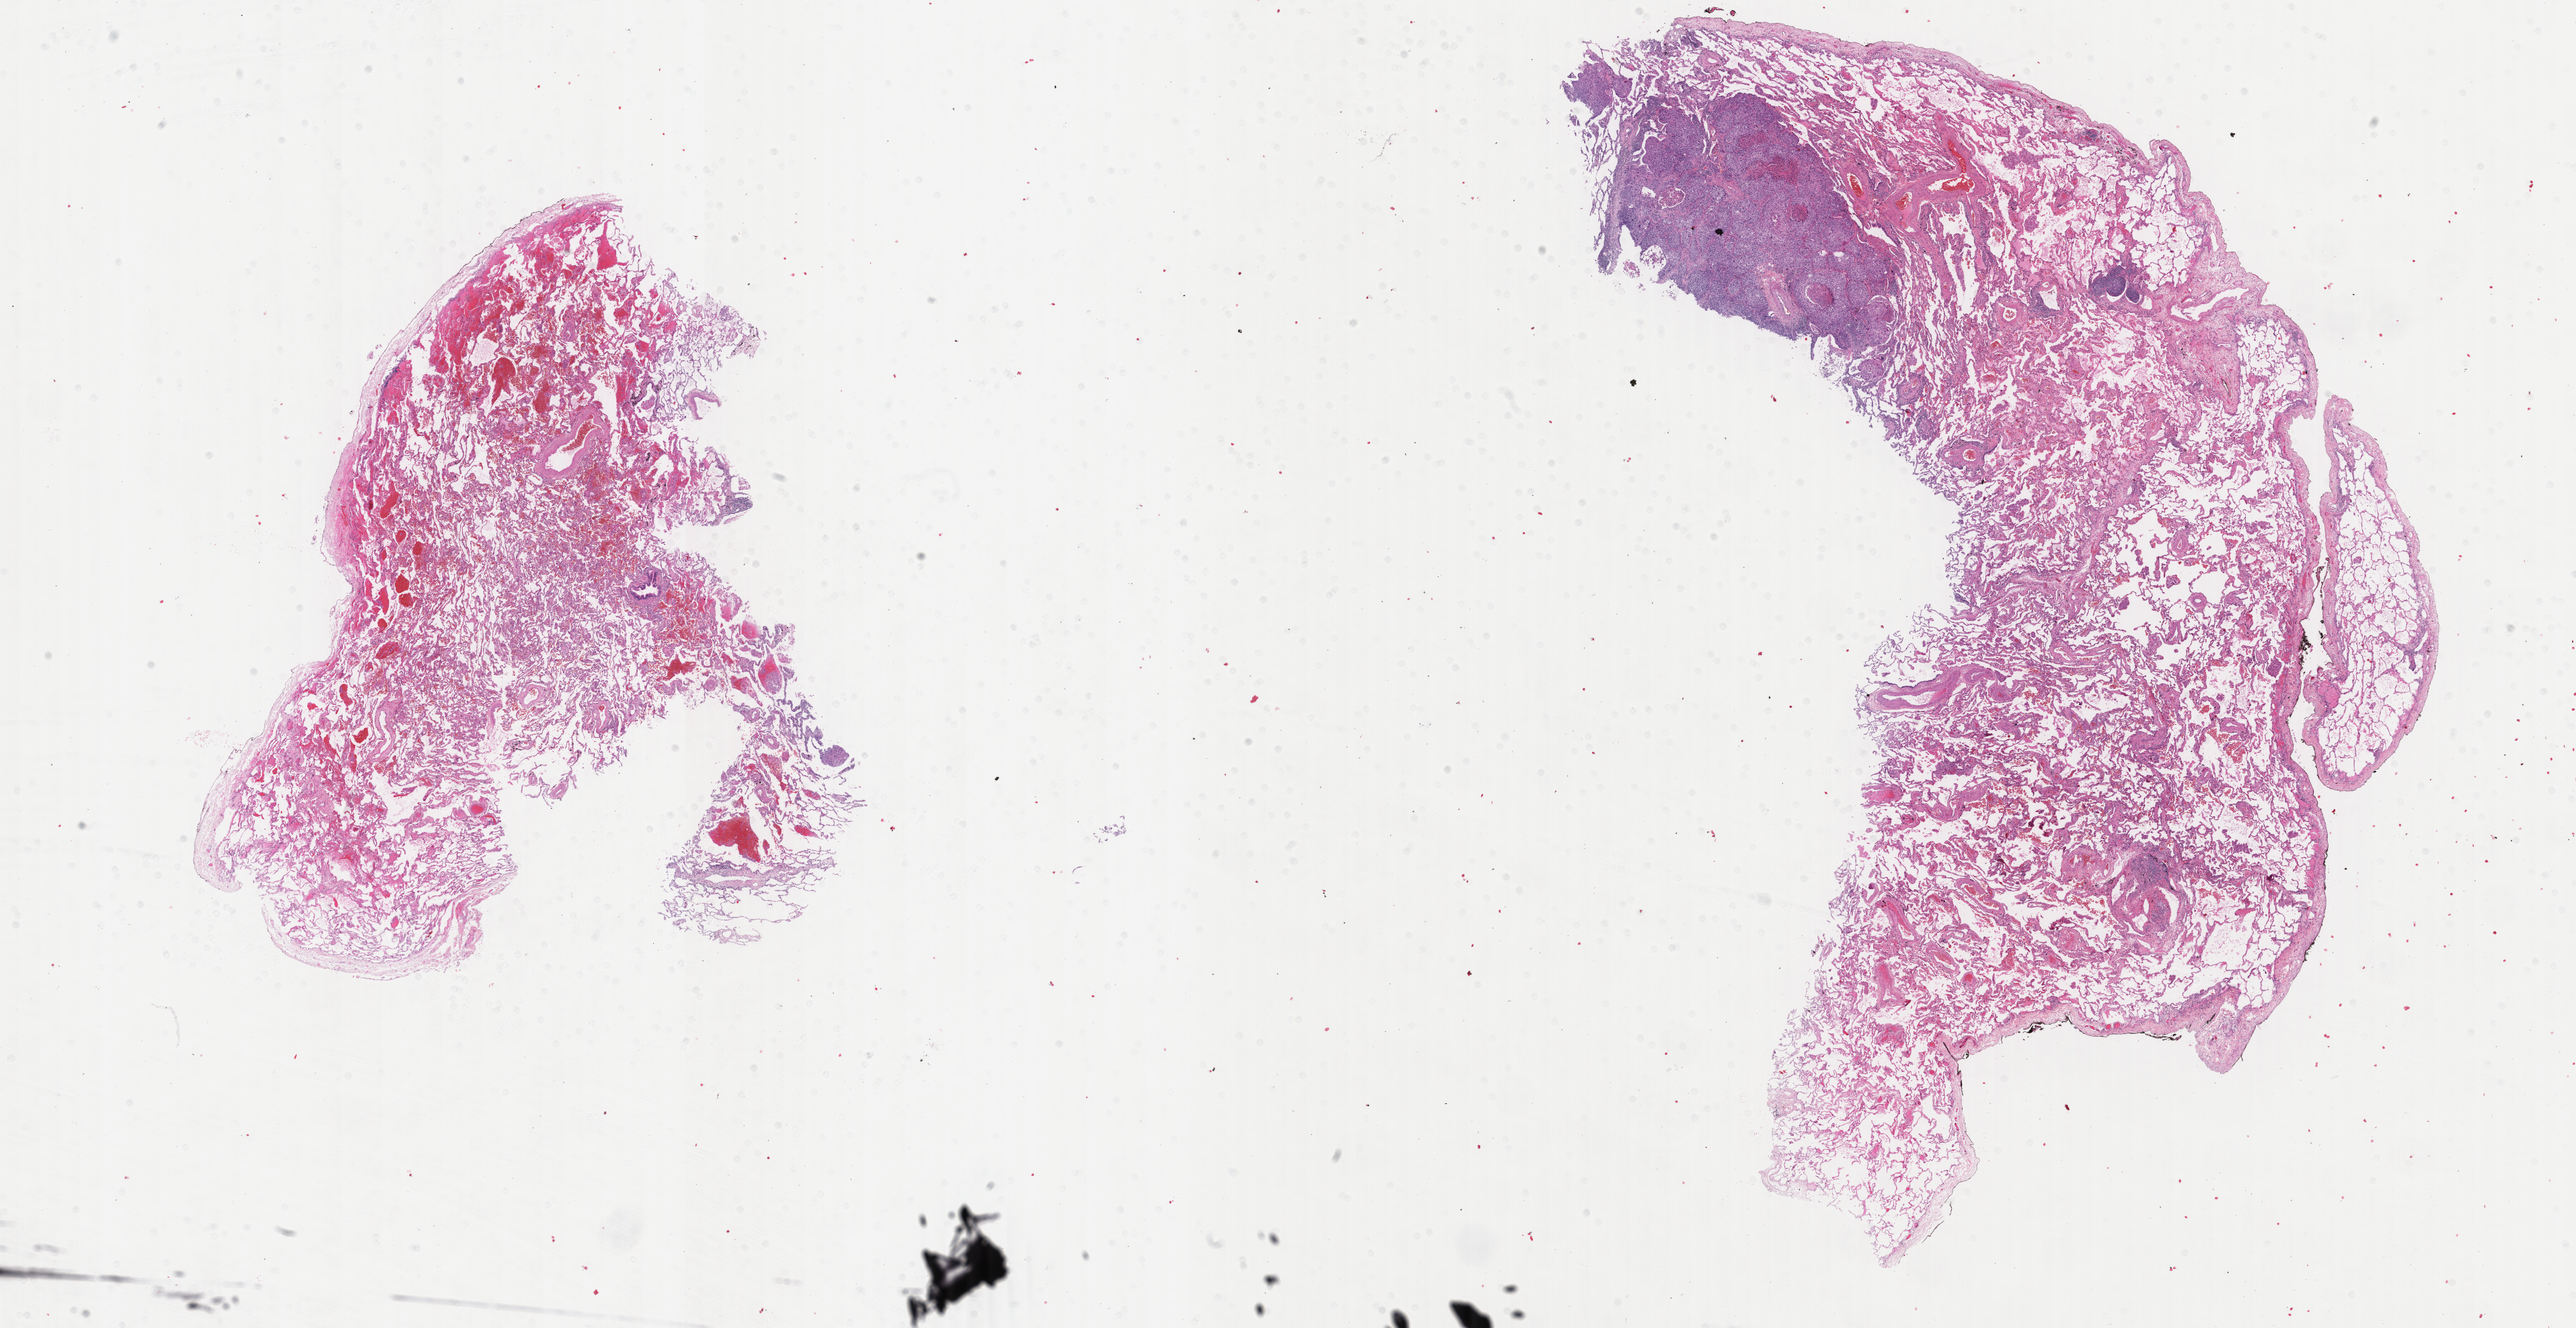
Digitized H&E tissue section (whole slide) — a low-resolution overview of the entire scanned area, about 30.5 x 15.7 mm; formalin-fixed paraffin-embedded (FFPE) diagnostic section; lung, primary tumour sample. Female patient; age at initial diagnosis 59 years.
Pathologic diagnosis: Squamous cell carcinoma, NOS (upper lobe, lung). AJCC pathologic stage: IA (5th edition).